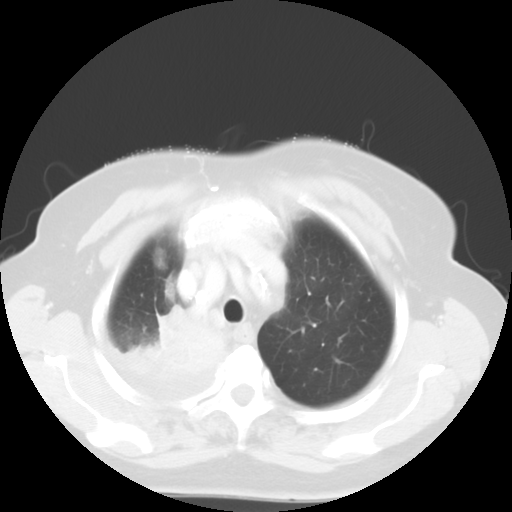
Chest CT, one axial slice; position 44 of 52 along the scan axis; reconstruction kernel STANDARD; 120 kVp; lung window (W 1500 / L -600 HU); 5 mm slice thickness; 512 × 512 image matrix. Patient: female, 81 years. Case-level facts recorded for this patient, not image findings: clinical TNM (as recorded): T4 N3 M1b.
Outlined on this slice (bounding box drawn by a radiologist):
- lung tumour (recorded histology: adenocarcinoma): bounding box <117,302,227,391> (left, top, right, bottom; pixels)